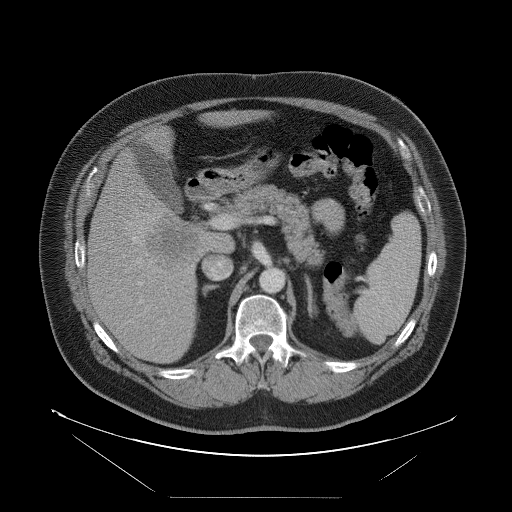
Contrast-enhanced abdominal CT, one axial slice. Slice 53 of 114 in the series (ordered by position). Soft-tissue window (W 400 / L 40 HU). 512 × 512 image matrix. Male patient, age 61 years. Case-level facts recorded for this patient, not image findings: diagnosis: colorectal cancer liver metastases, imaged before liver resection; multiple liver metastases: no; largest metastasis: 6.5 cm; disease in both lobes: yes.
Outlined on this slice (expert manual segmentation):
- hepatic veins: bounding box [x1, y1, x2, y2] px = [133, 237, 136, 240]
- liver: [89, 111, 257, 363]
- planned liver remnant (the part of the liver to remain after resection): [144, 111, 262, 160]
- liver metastasis: [146, 216, 197, 271]